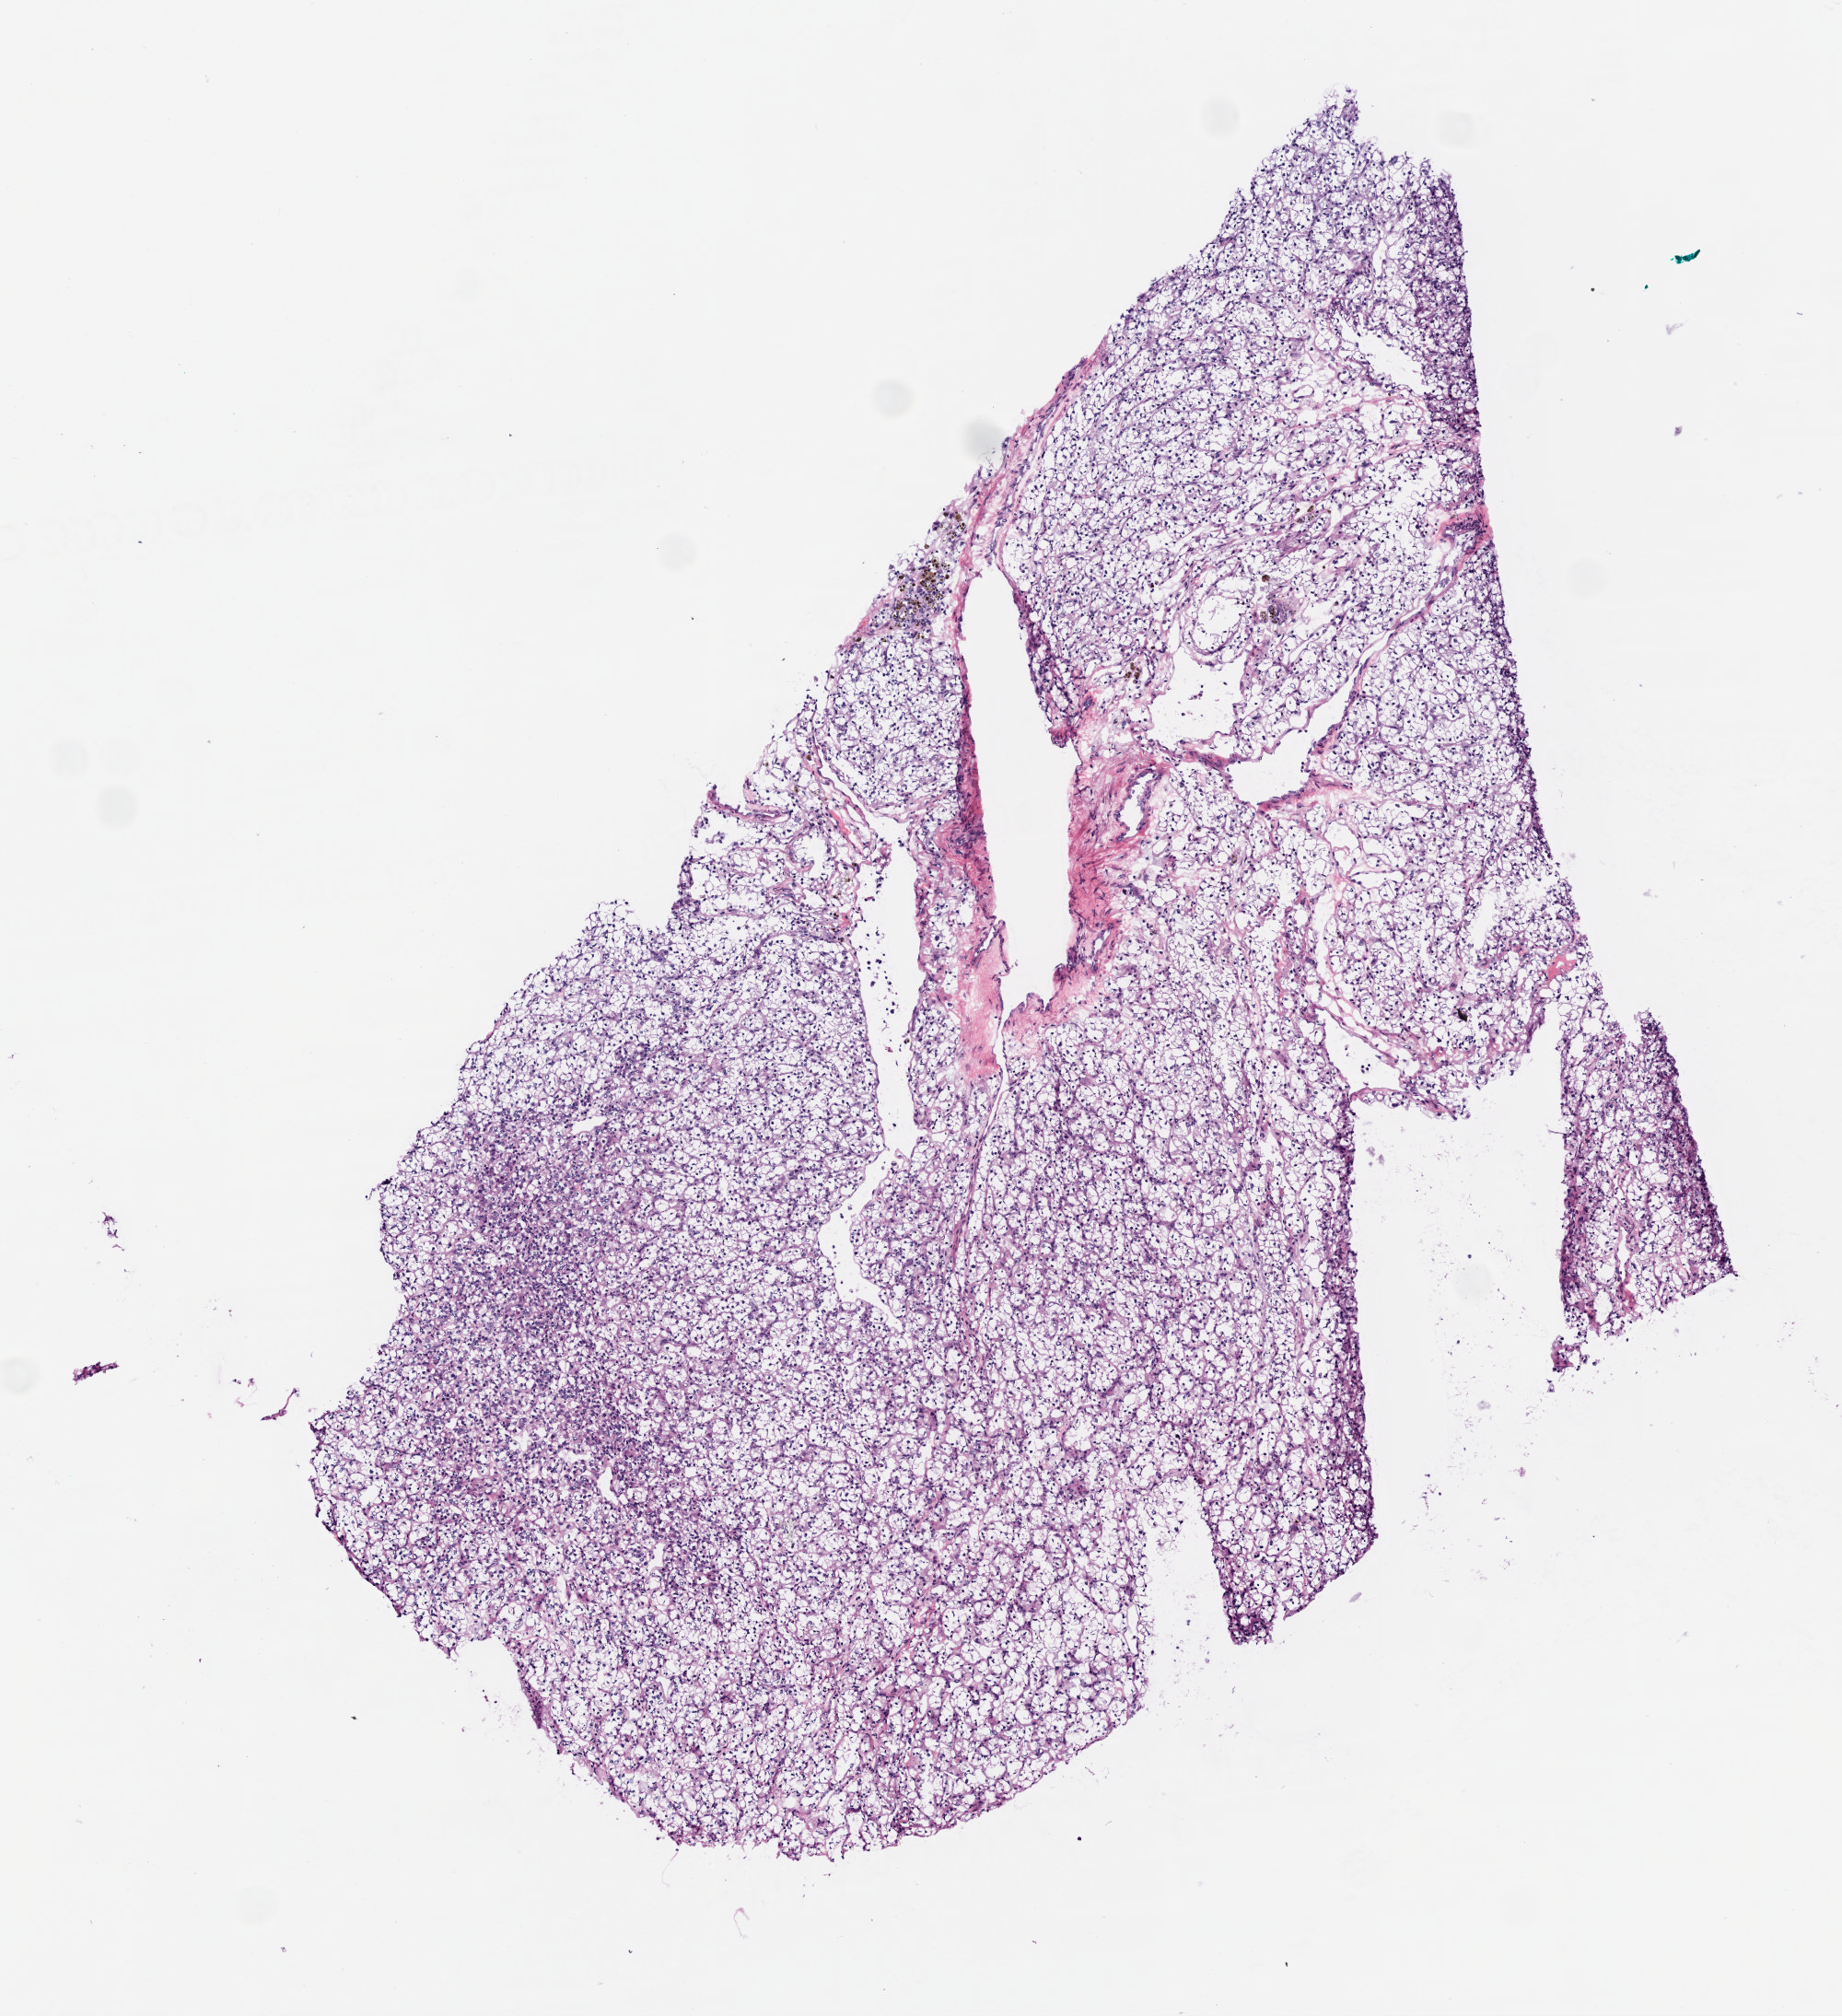
Whole-slide histology image, H&E — whole scanned area (about 4.0 x 4.4 mm, from a 20x scan) shown as a low-resolution overview. Frozen section. Primary tumour sample from the kidney. Patient: male, age at initial diagnosis 58 years. Histologic grade: G2 (moderately differentiated). Slide review estimates, as recorded: tumour cells 97%, tumour nuclei 71%, normal cells 0%, stromal cells 3%, necrosis 0%.
- AJCC pathologic stage: I (6th edition)
- diagnosis: Clear cell adenocarcinoma, NOS
- TNM: T1a NX M0
- laterality: right